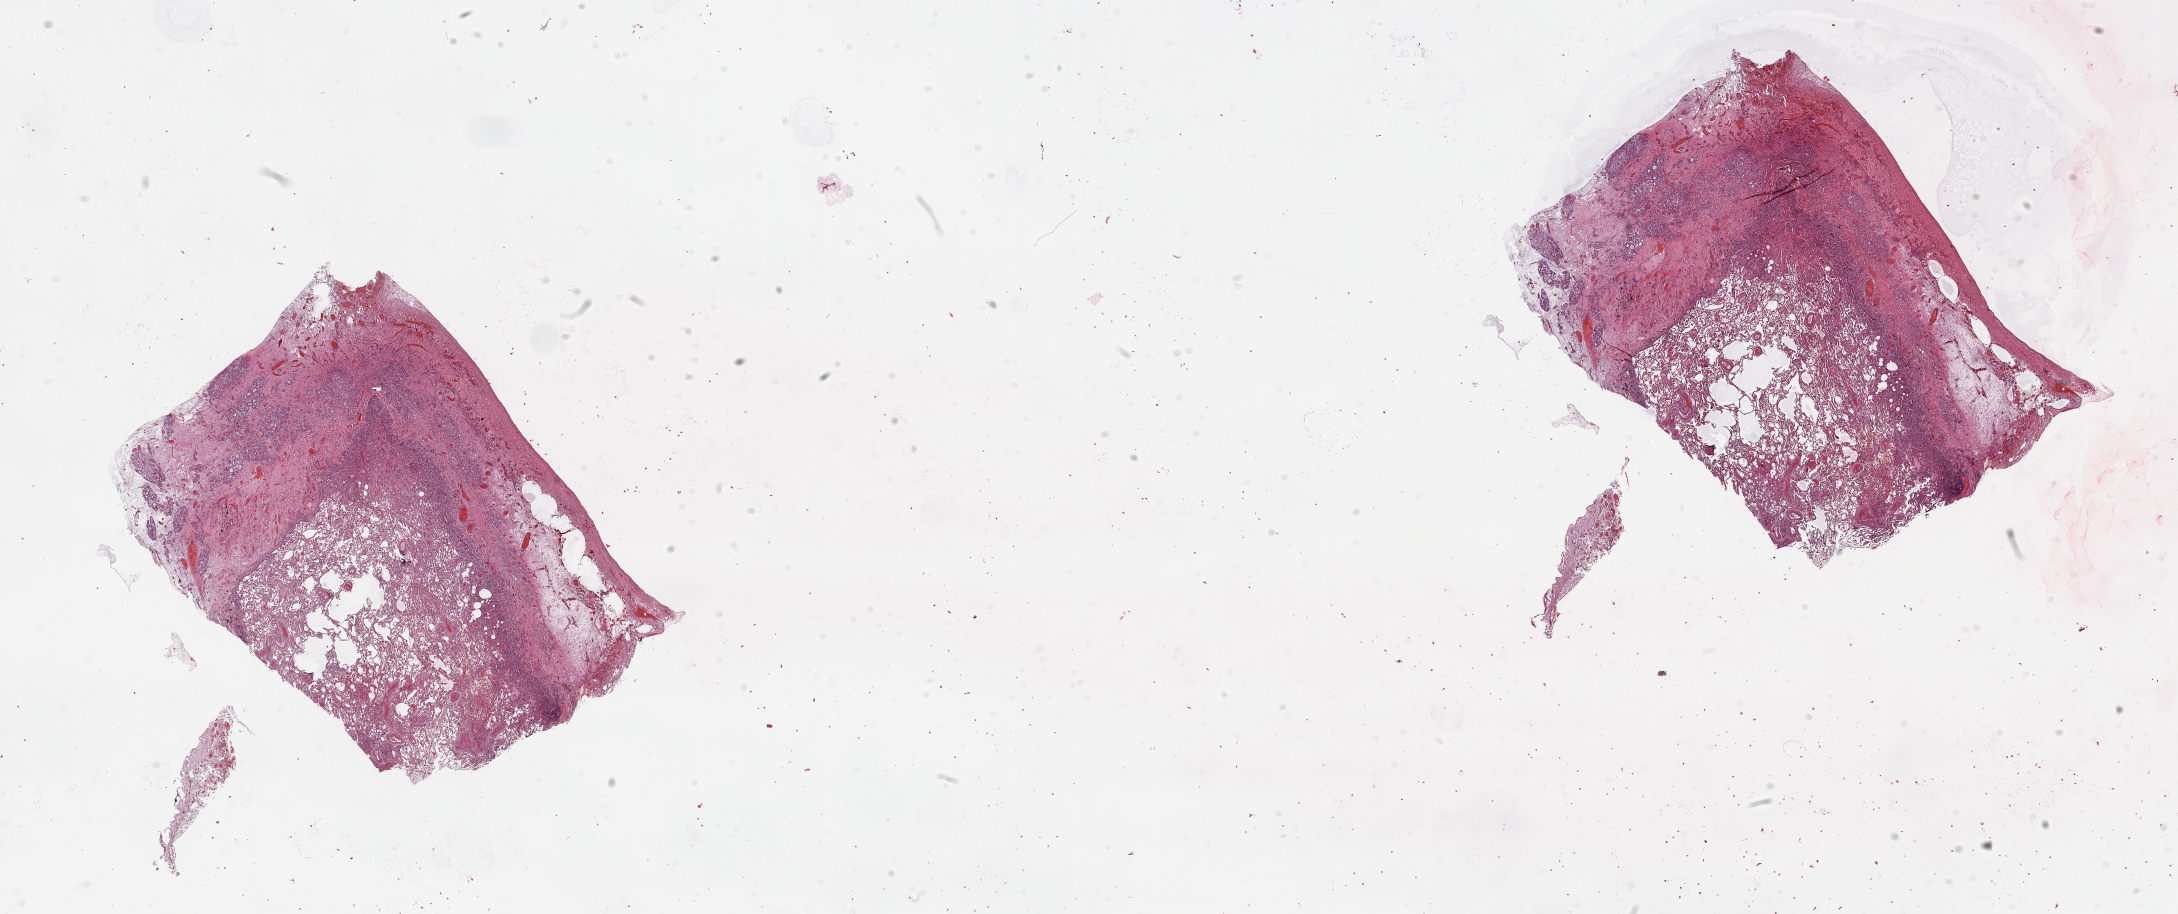
Whole-slide histology image, H&E-stained — low-resolution overview of the scanned area, about 34.5 x 14.5 mm (acquisition: 20x scan). Normal (non-tumour) tissue sample, lung. 73-year-old male patient.
* this section: normal (non-tumour) tissue from the same patient
* patient diagnosis: Squamous cell carcinoma, NOS